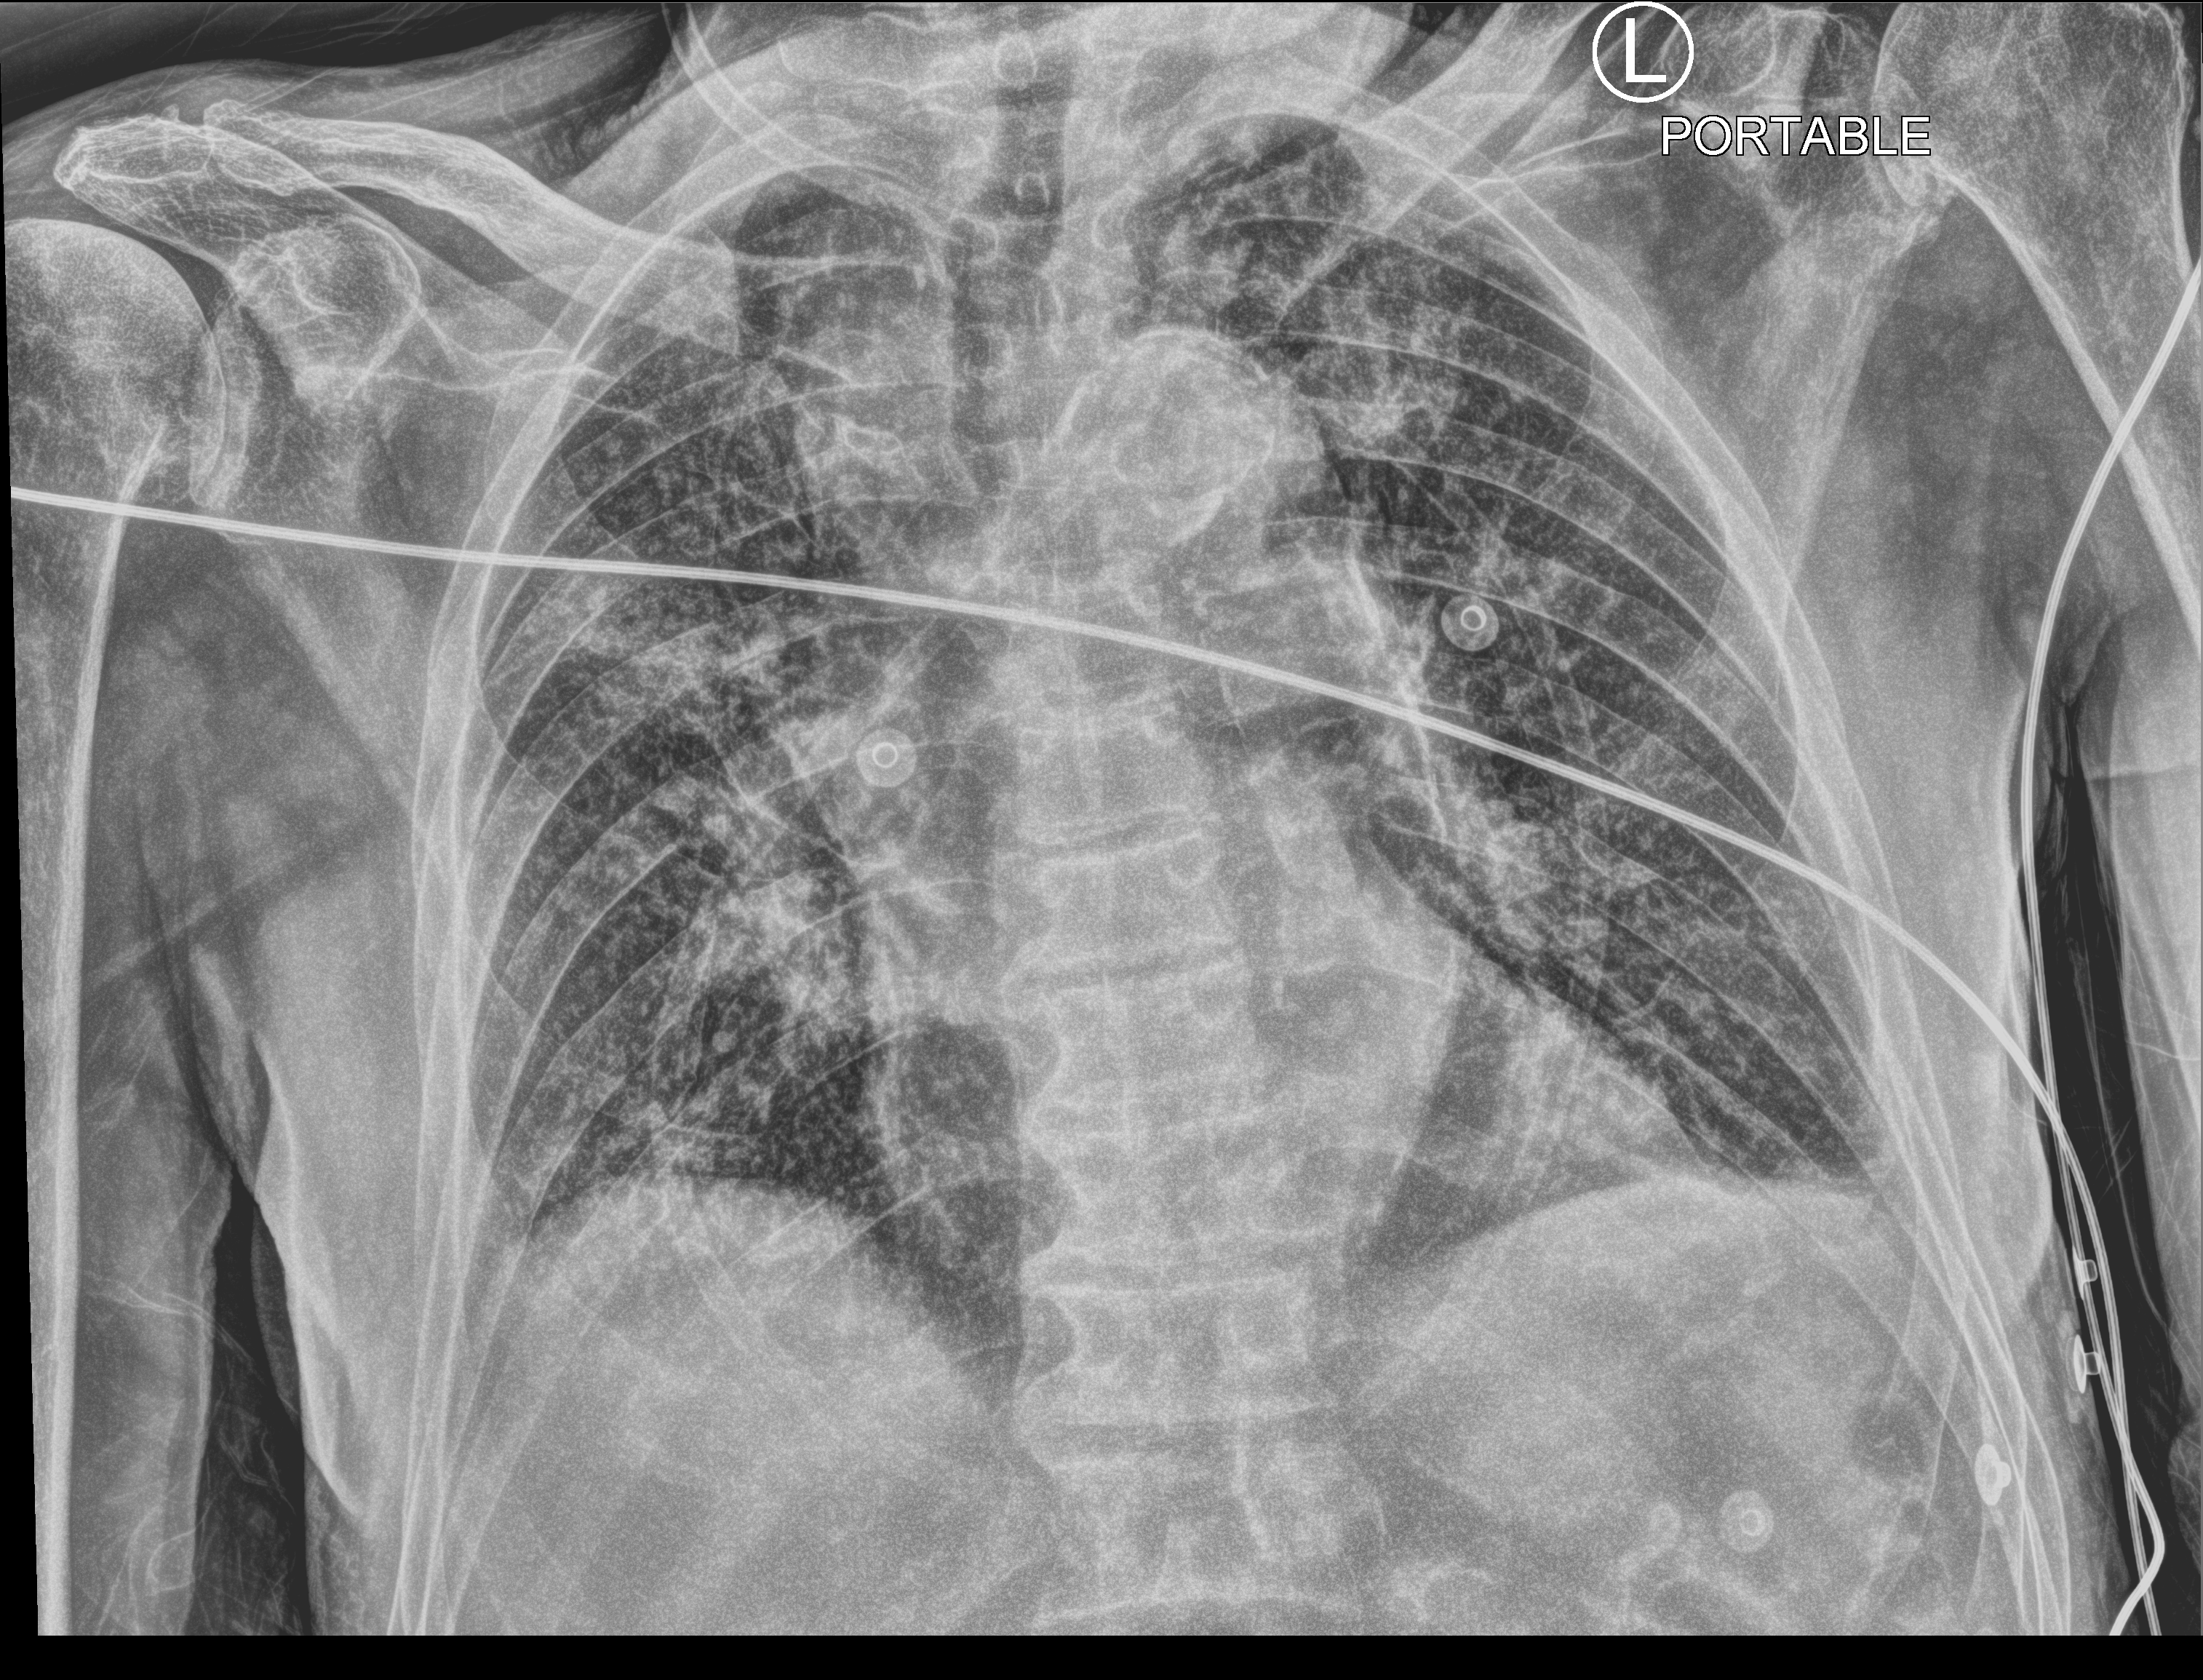
Bedside chest radiograph (computed radiography); anteroposterior (AP) projection. Male patient hospitalised with COVID-19, age 75–90 years.
Hospital-stay facts (about this admission, not read from this image; timing relative to this image not recorded): admitted to intensive care during this hospital stay: no; mechanically ventilated during this hospital stay: no; hypertension (admission record): yes.